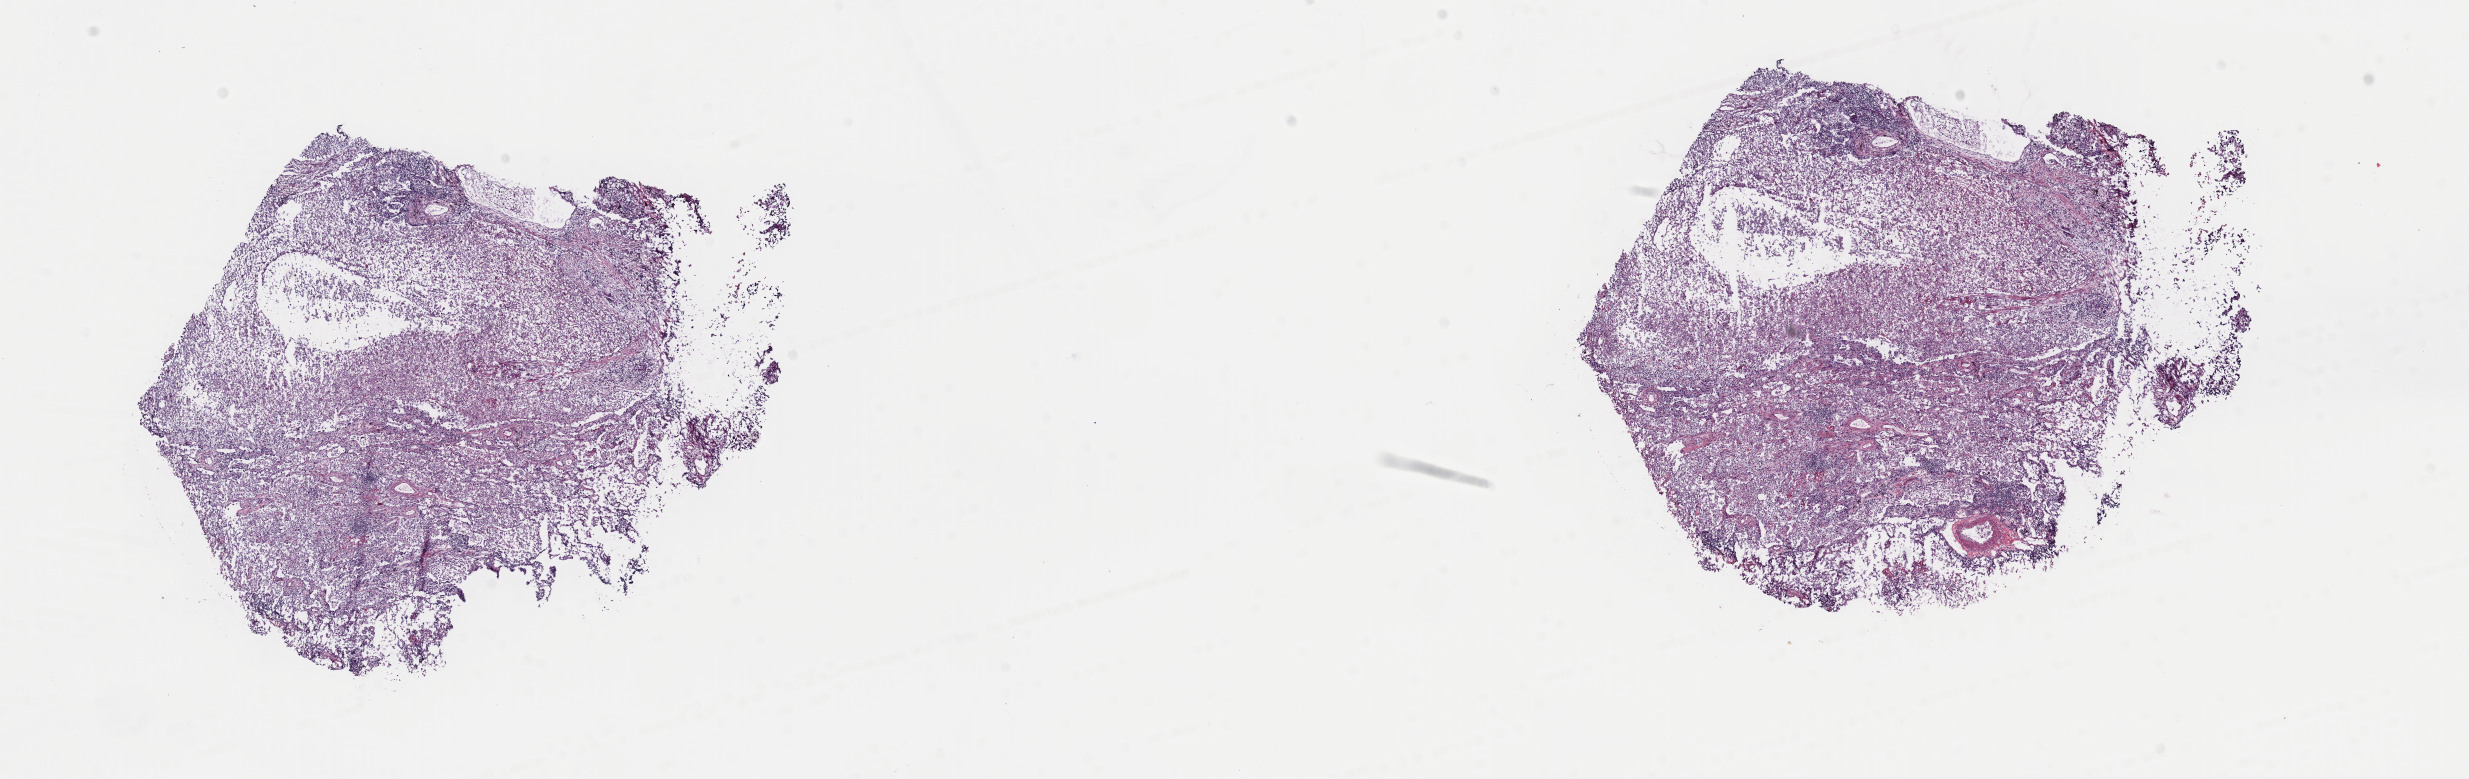
Whole-slide histology image, H&E, low-resolution overview of the scanned area, about 19.5 x 6.2 mm; frozen section from the top of the tissue portion; sample: primary tumour, lung. Patient: male, age at initial diagnosis 64 years. Slide review estimates, as recorded: tumour cells 60%, tumour nuclei 60%, normal cells 0%, stromal cells 38%, necrosis 2%. Inflammatory infiltration, as recorded: lymphocyte infiltration 7%, monocyte infiltration 5%, neutrophil infiltration 3%.
• AJCC pathologic stage: IIIB (6th edition)
• TNM: T4 N0 M0
• laterality: left
• diagnosis: Papillary squamous cell carcinoma (upper lobe, lung)